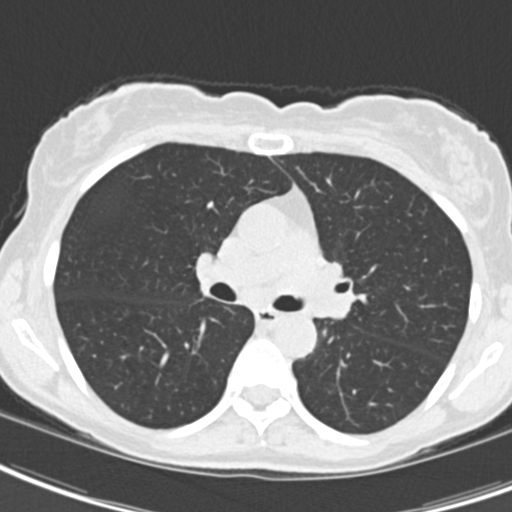
Low-dose screening chest CT, one axial slice. Slice 122 of 189 in the series (ordered by position). Reconstruction kernel B30f. Lung window (W 1500 / L -600 HU). 2 mm slice thickness. 512 × 512 image matrix.
Annotated regions visible in this slice (manually delineated by an expert):
- lesion 2 (tumor, hilum of left lung): bounding box [x1, y1, x2, y2] px = [294, 263, 354, 318]